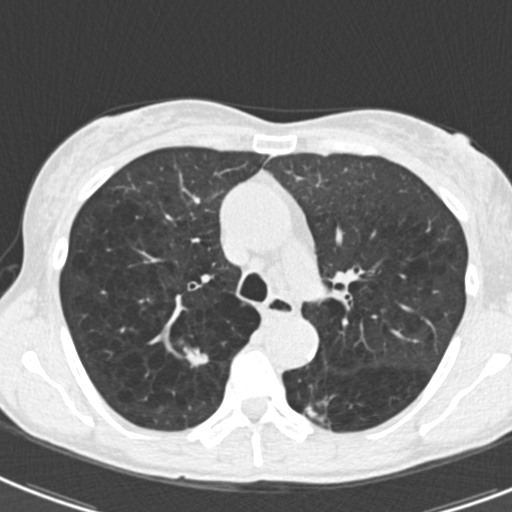
Low-dose screening chest CT, axial slice. Second screening round (one year after baseline). Lung window (W 1500 / L -600 HU). 2 mm slice thickness. 512 × 512 image matrix. Female, age 61 years at enrolment. Current smoker at enrolment.
Expert reader's lesion annotation, bounding box [x1, y1, x2, y2] px = [171, 335, 224, 382]. Screening reader's record for this exam (one nodule recorded; not confirmed to be the boxed lesion): non-calcified nodule or mass ≥4 mm, right upper lobe, 12 × 6 mm, smooth margins, soft tissue attenuation, pre-existing on the prior screen: yes; interval growth: yes. Participant outcome: lung cancer diagnosed 455 days after this screen (after the third annual screen) — non-small cell carcinoma, right upper lobe, undifferentiated (G4), stage IA (AJCC 6th edition), 15 mm at pathology.